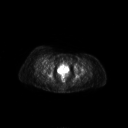
FDG PET of an extremity soft-tissue mass (from a PET/CT study), one axial slice; 128 × 128 image matrix, field of view 700 × 700 mm. Patient: female, 56 years. Case-level facts recorded for this patient, not image findings: histological type: malignant solitary fibrous tumor; grade: intermediate; site of the primary tumour: right thigh.
Outlined on this slice (expert contour drawn on MRI and transferred to this co-registered scan by the dataset authors):
- gross tumour volume including surrounding oedema: box from (x=38, y=57) to (x=44, y=62) px